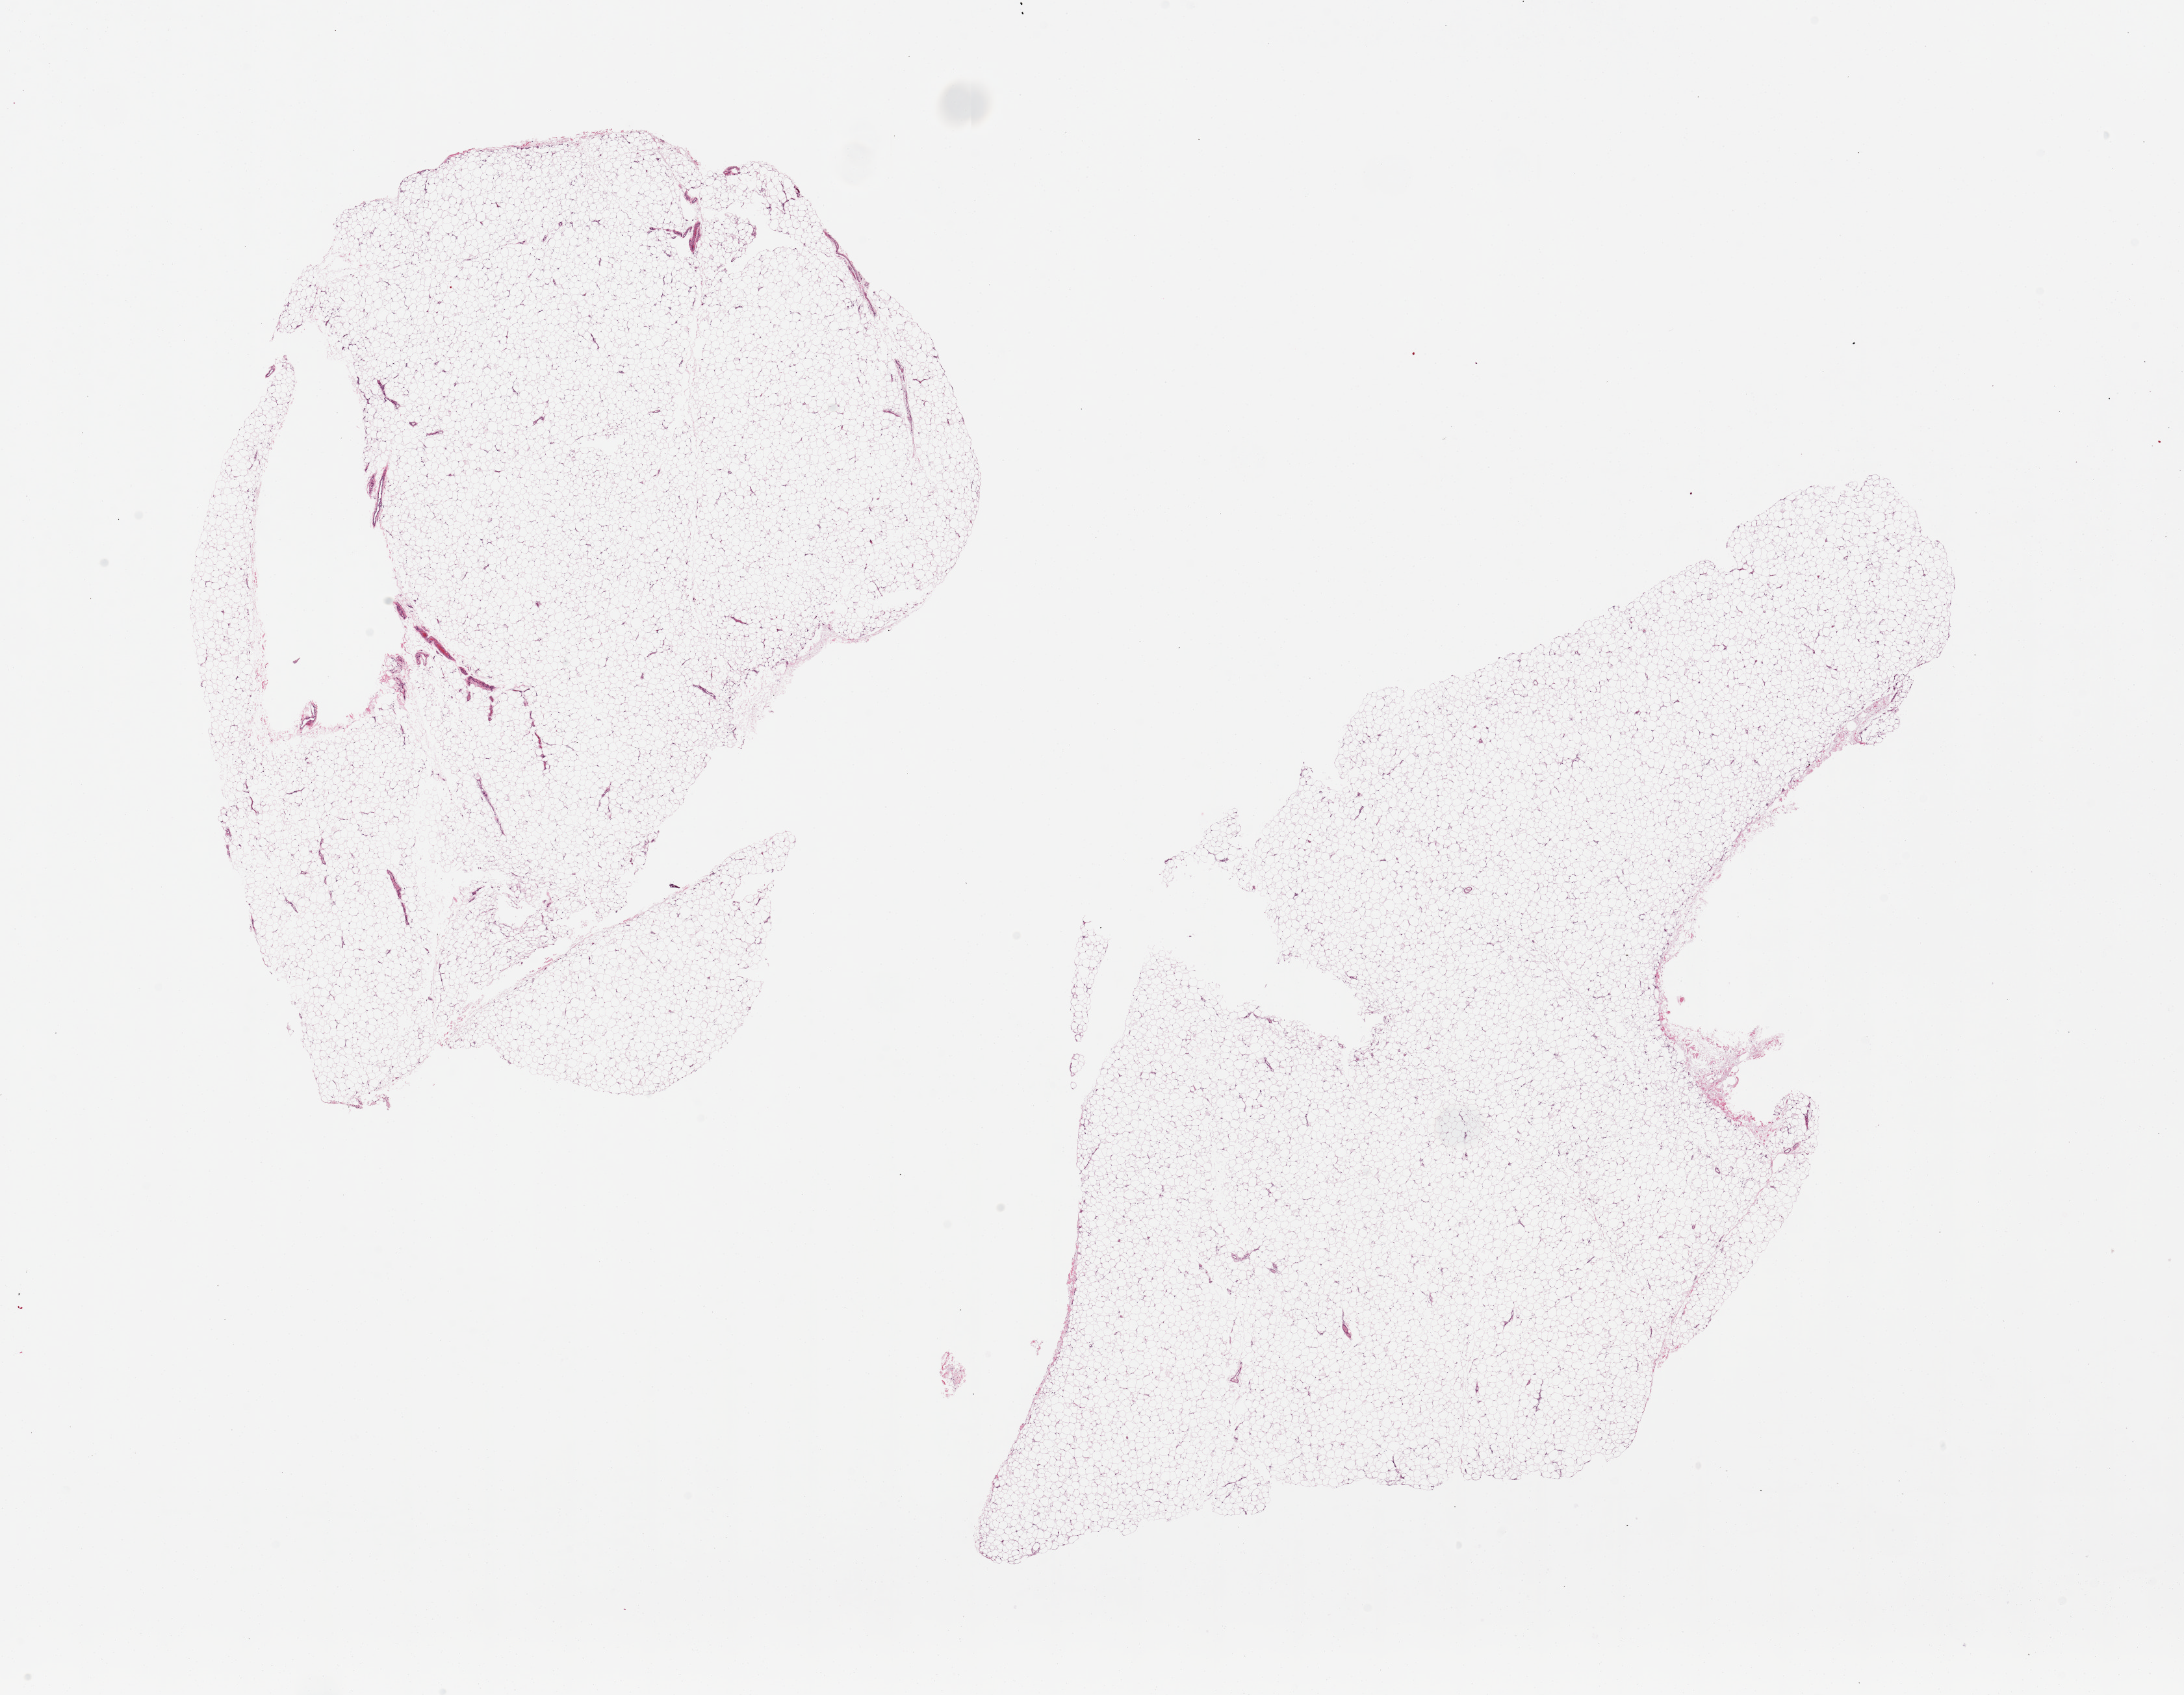
Digitized hematoxylin and eosin (H&E)-stained section — shown as a low-resolution overview of the whole scanned area (about 26.6 x 20.6 mm). PAXgene-fixed paraffin-embedded (PFPE) section. Sampled site (target tissue): adipose tissue. Donor tissue sample. Donor: female.
Review note (as recorded): 2 pieces, 13x9.5 & 17x9mm.